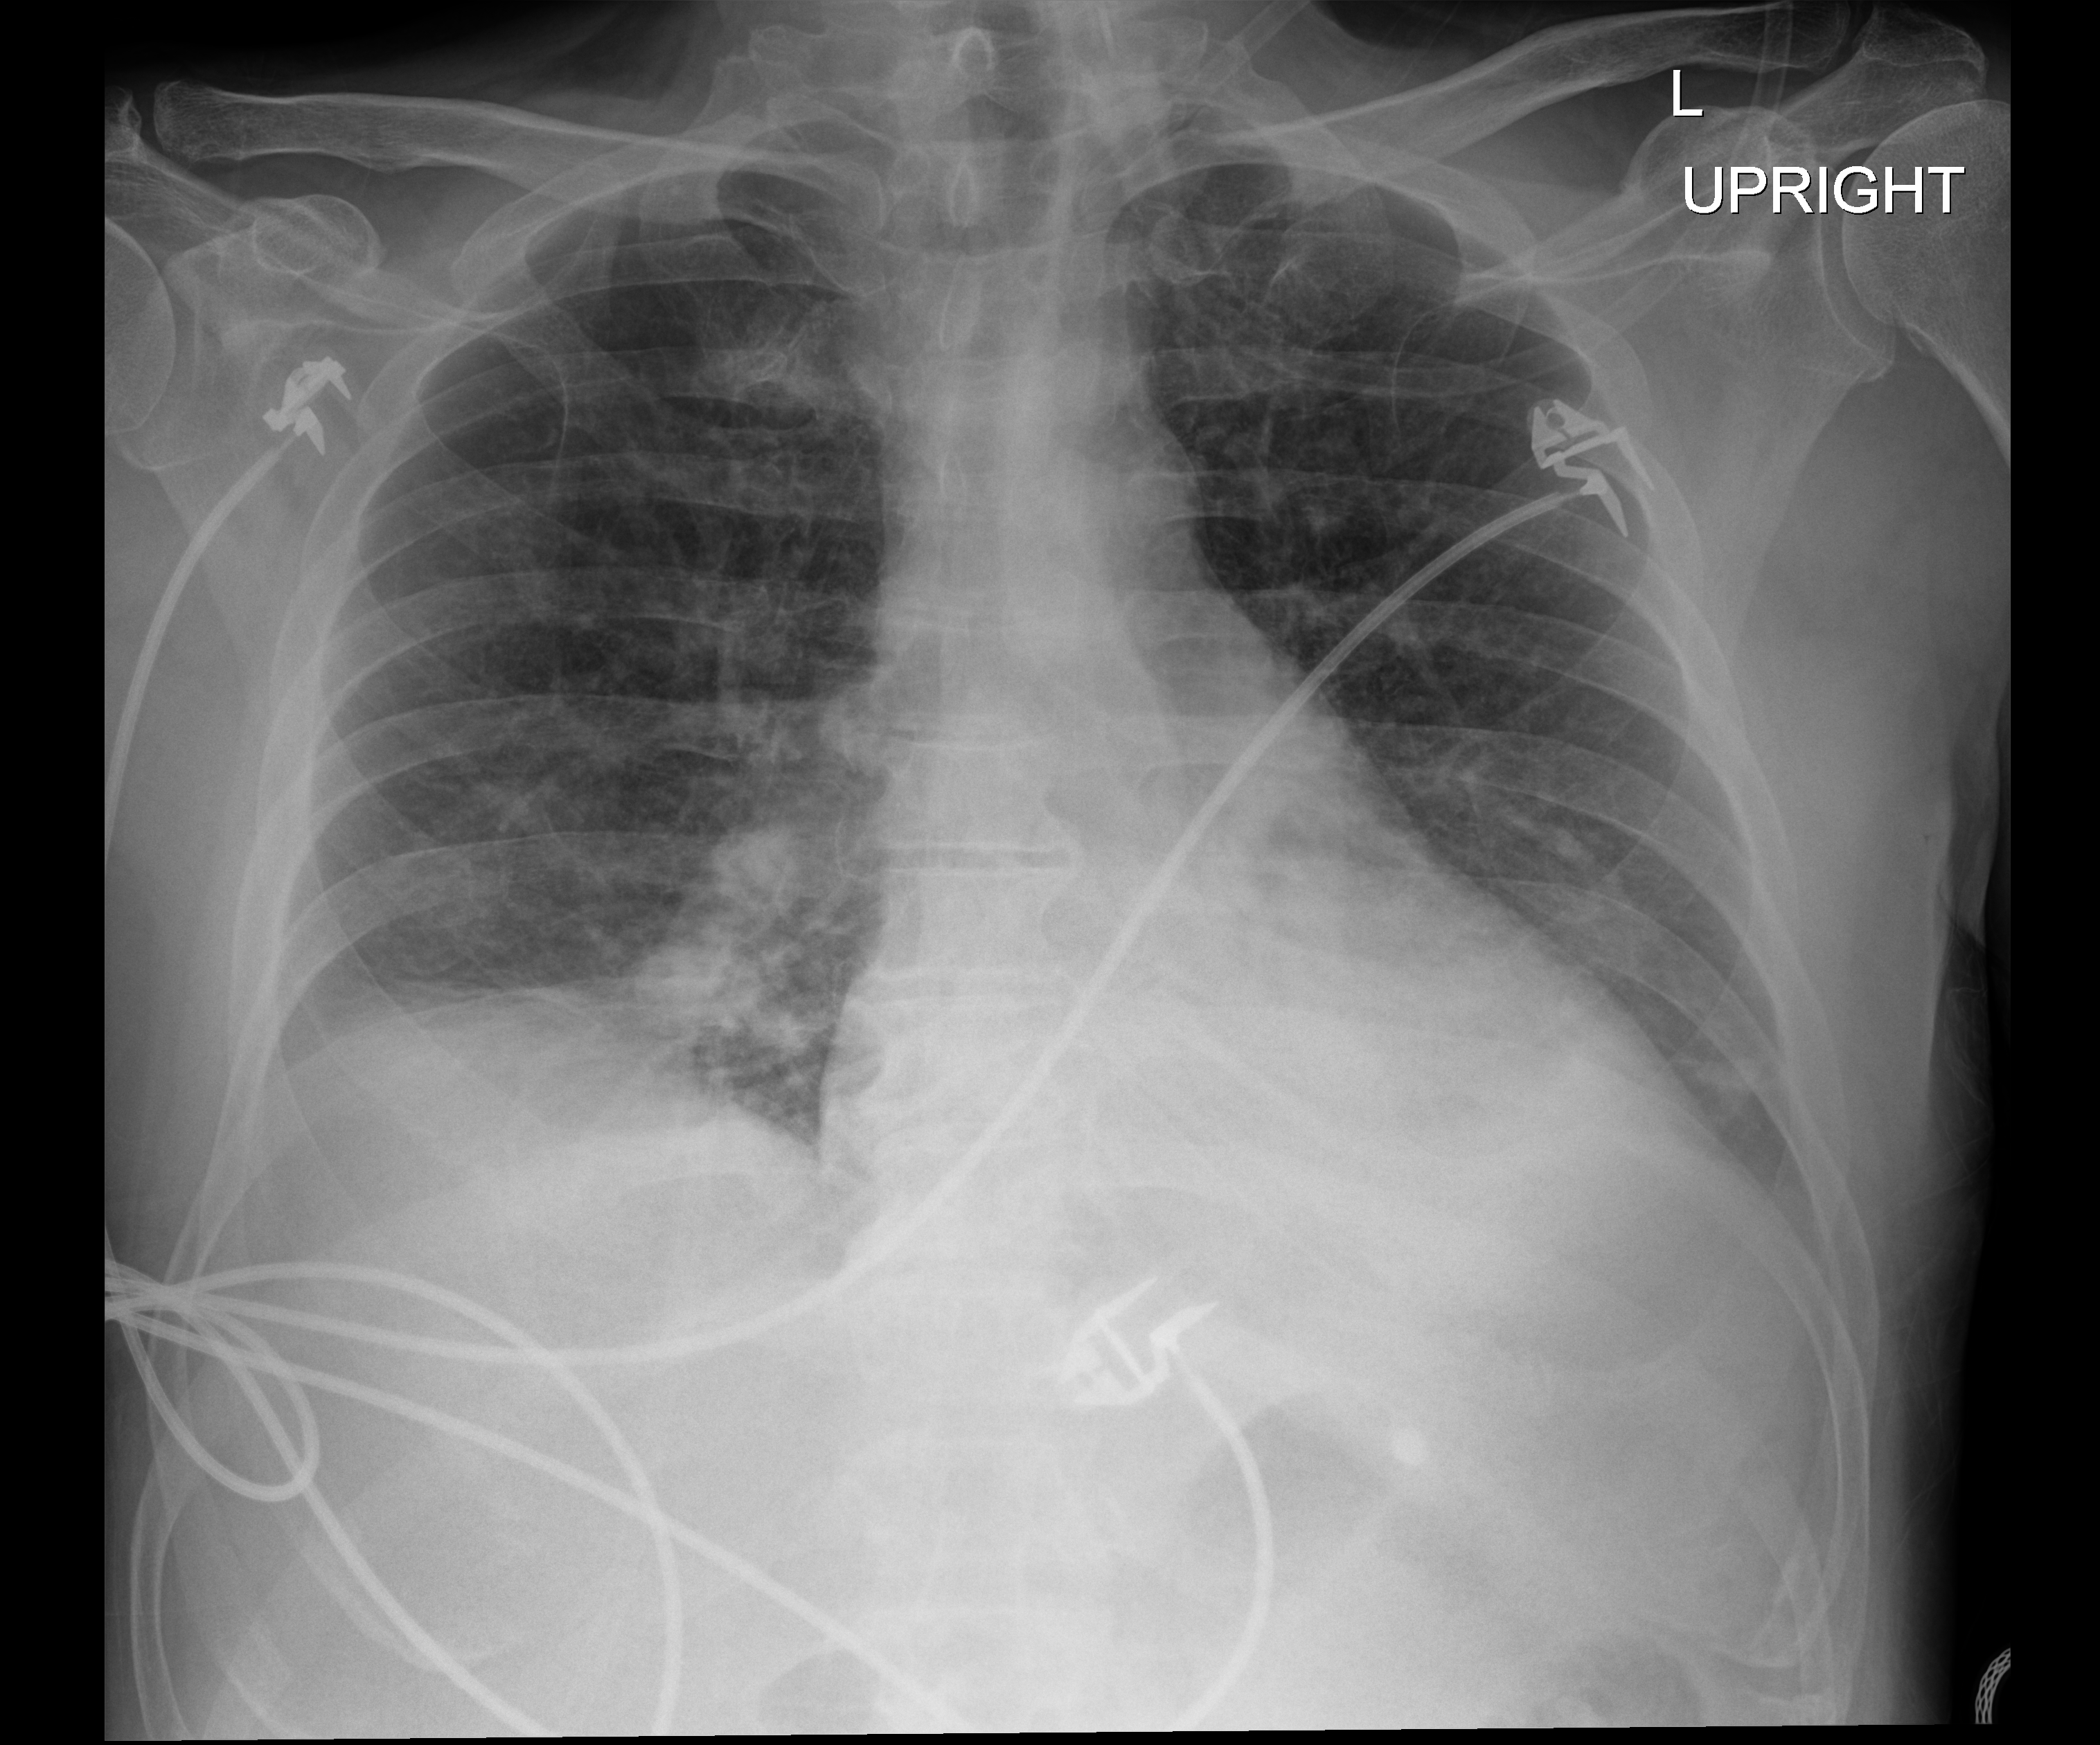
Chest radiograph, anteroposterior (AP) projection. Male patient hospitalised with COVID-19, age 18–59 years.
Hospital-stay facts (about this admission, not read from this image; timing relative to this image not recorded):
- mechanically ventilated during this hospital stay: no
- admitted to intensive care during this hospital stay: no